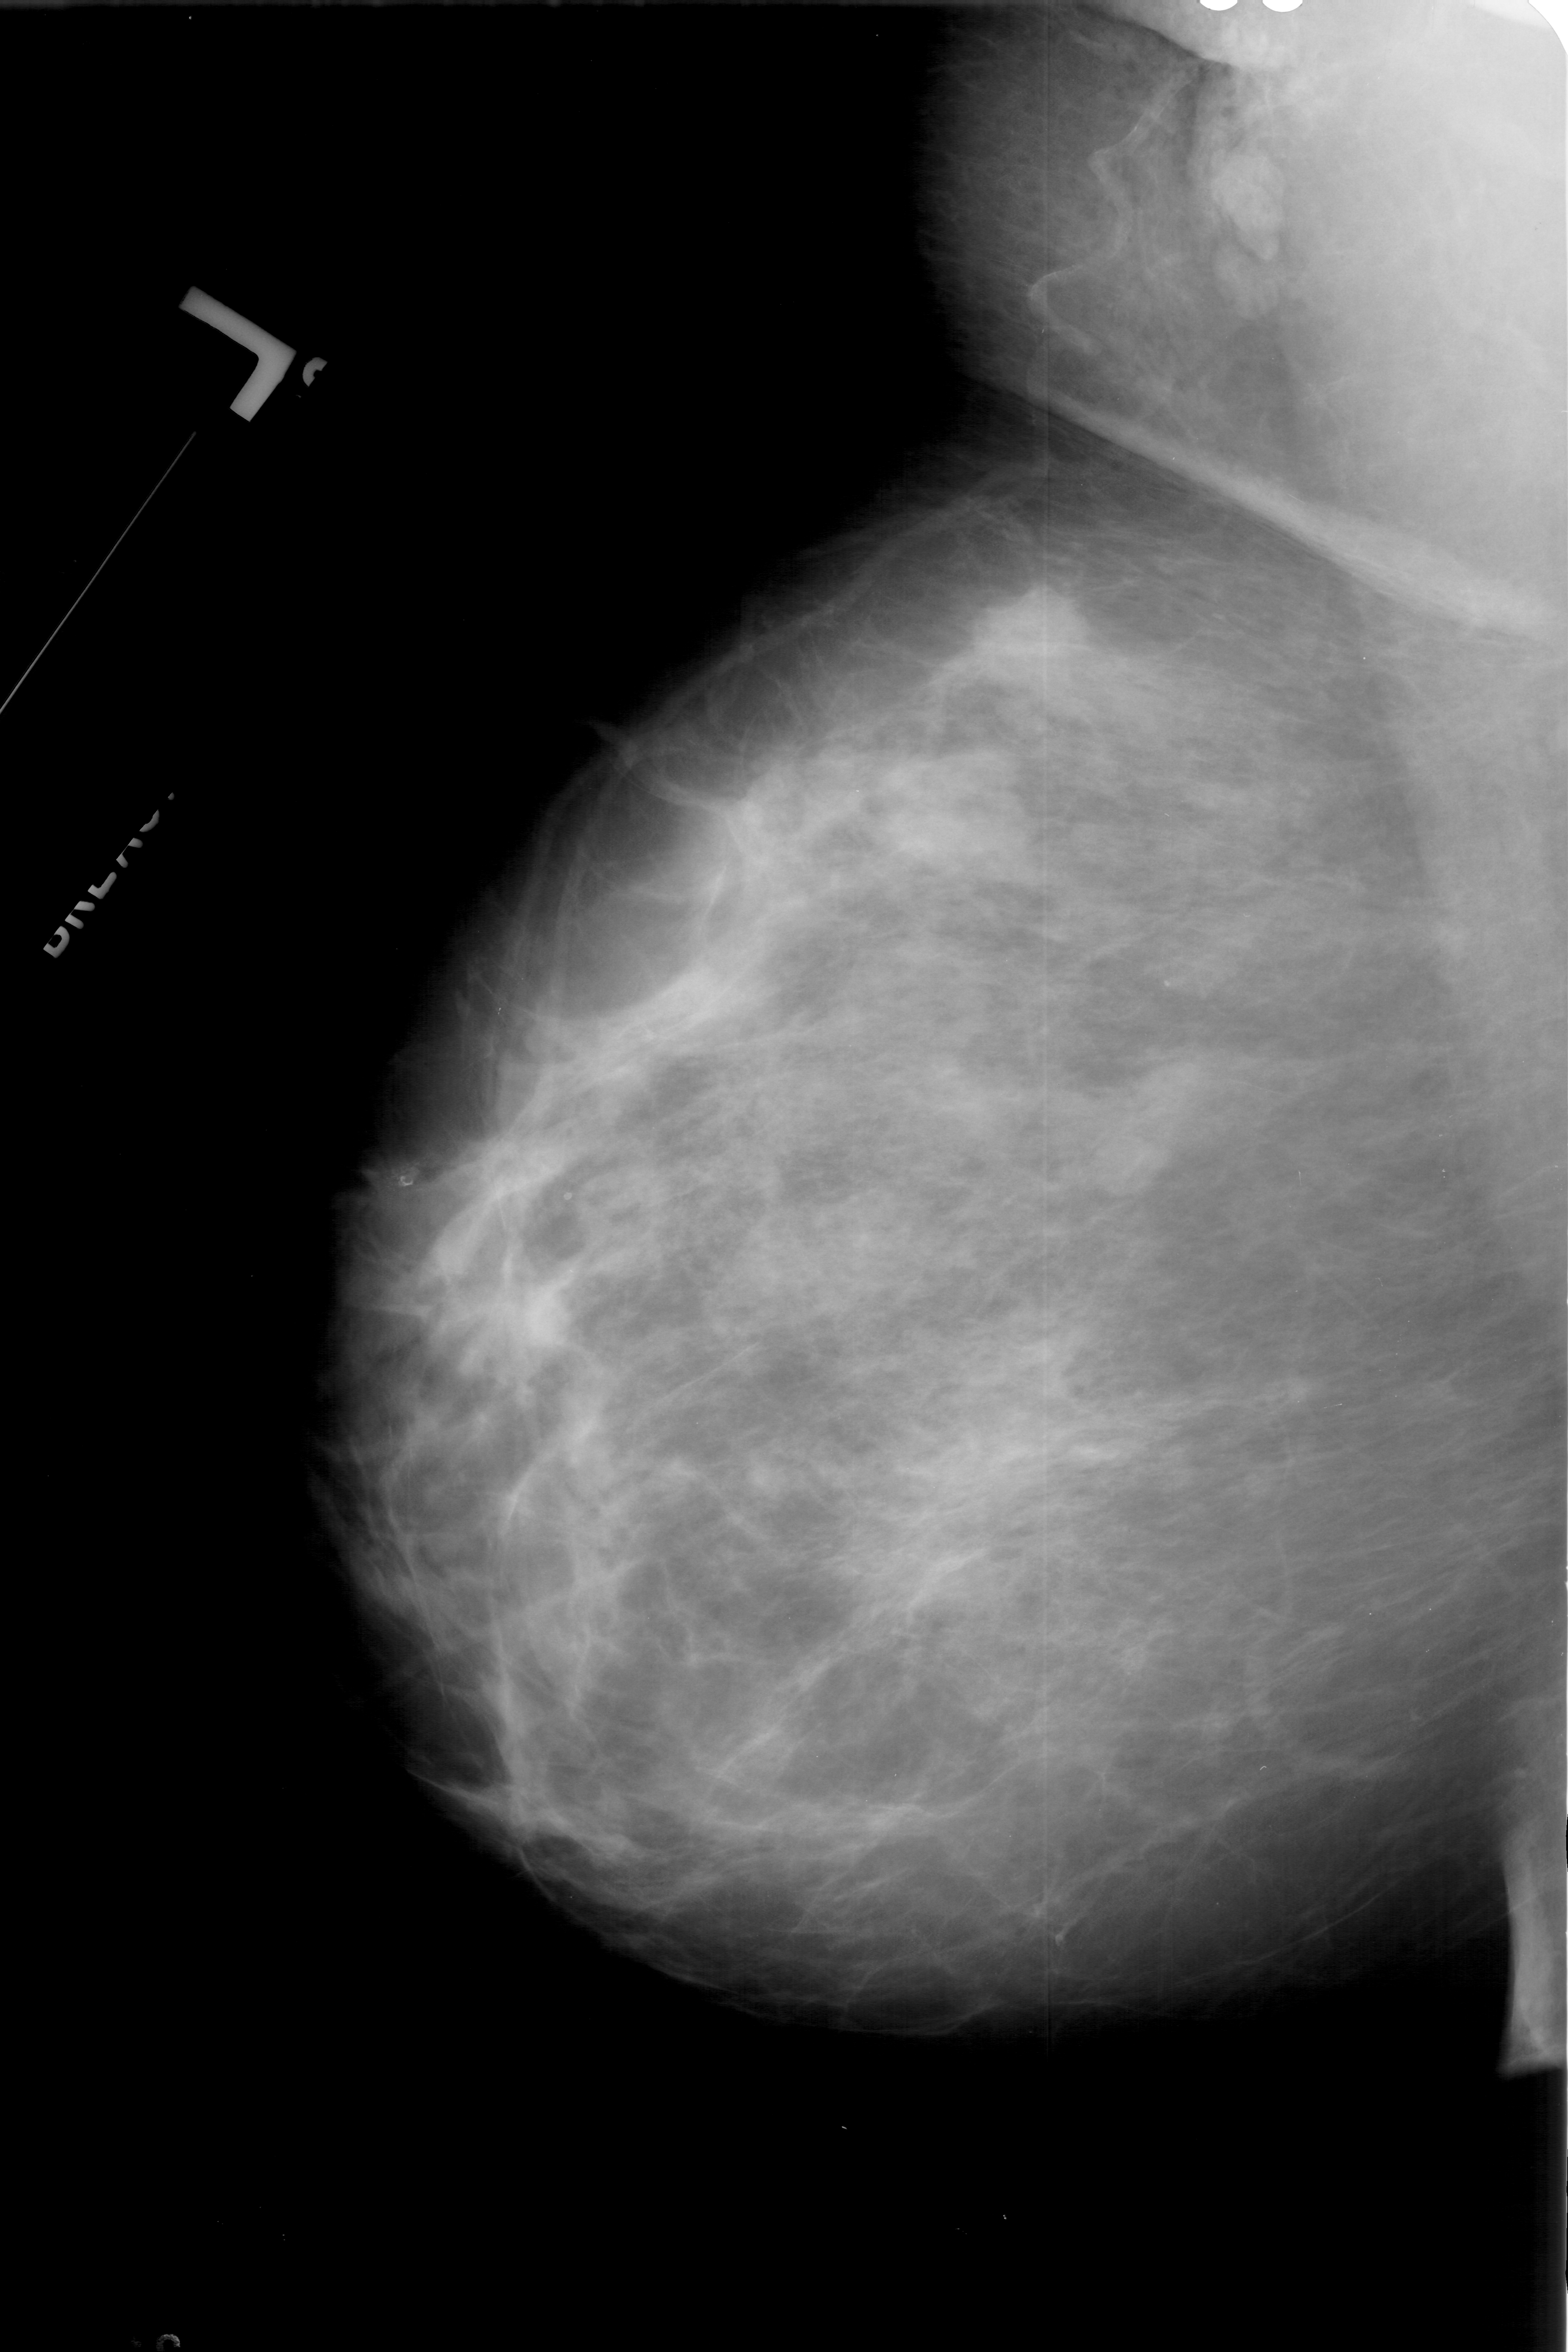
Scanned film-screen mammogram; left breast; MLO view; breast composition: heterogeneously dense (BI-RADS density category 3 of 4); 1568 × 2352 image matrix.
Expert-marked regions of interest on this image (one box per marked abnormality):
- mass, shape lobulated, margins ill defined; BI-RADS assessment category 4; subtlety rating 2 on a 1 (subtle) to 5 (obvious) scale; pathology (as recorded): malignant: box from (x=963, y=582) to (x=1066, y=672) px